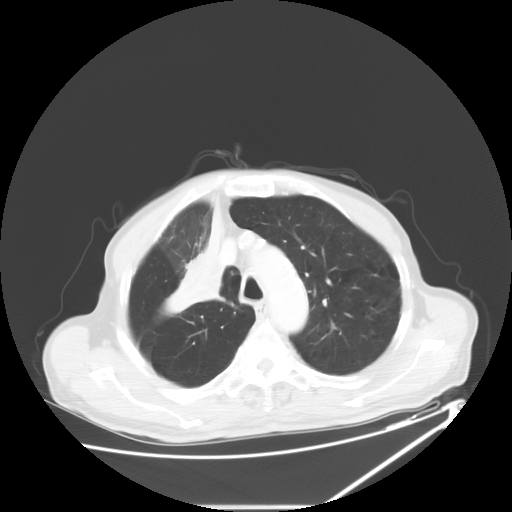
Chest CT, one axial slice; position 47 of 60 along the scan axis; reconstruction kernel STANDARD; 120 kVp; lung window (W 1500 / L -600 HU); 512 × 512 image matrix, field of view 410 × 410 mm. Male patient, age 73 years. Case-level facts recorded for this patient, not image findings: clinical TNM (as recorded): T2a N1 M0.
Outlined on this slice (bounding box drawn by a radiologist):
- lung tumour (recorded histology: squamous cell carcinoma): bounding box [x1, y1, x2, y2] px = [162, 205, 228, 314]